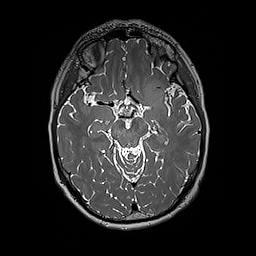
Brain MRI from a brain-tumour surgery series, one axial slice; position 114 of 192 along the scan axis; 1 mm slice thickness; 256 × 256 image matrix, field of view 250 × 250 mm. Case-level facts recorded for this patient, not image findings: histopathology: Glioblastoma; WHO grade: 4; IDH mutation: no.
Structures marked on this image (manually delineated by an expert):
- tumour: bounding box (x1, y1, x2, y2) in pixels: (140, 80, 171, 111)